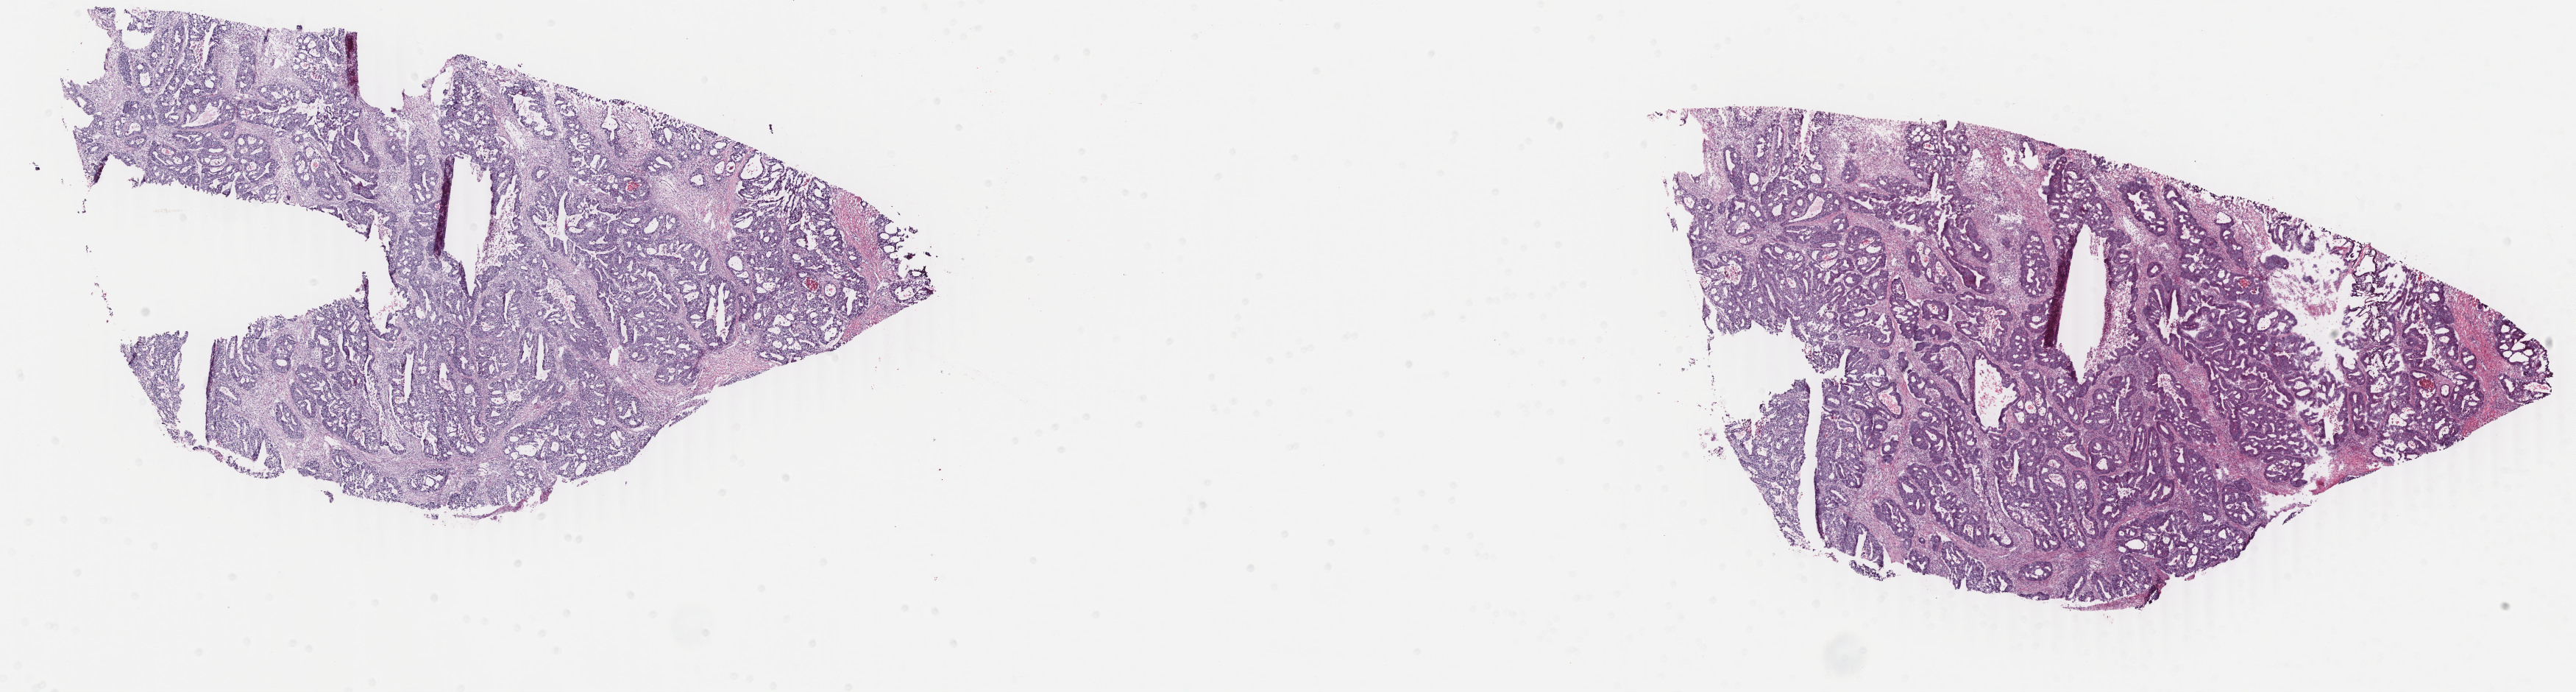
Digitized H&E-stained tissue section (whole slide) — low-resolution overview of the scanned area, about 27.8 x 7.5 mm (slide scanned at 40x). Frozen section from the bottom of the tissue portion. Primary tumour sample from the rectum. Female, age 57 years at initial diagnosis. Pathologist review of this section (percent, as recorded): tumour cells 85%, tumour nuclei 85%, normal cells 0%, stromal cells 0%, necrosis 15%. Infiltration values recorded for this section: lymphocyte infiltration 0%, monocyte infiltration 0%, neutrophil infiltration 0%.
- pathologic diagnosis: Adenocarcinoma, NOS (rectosigmoid junction)
- AJCC pathologic stage: IIA
- TNM: T3 N0 M0
- lymph nodes positive (case pathology): 0 of 14 examined